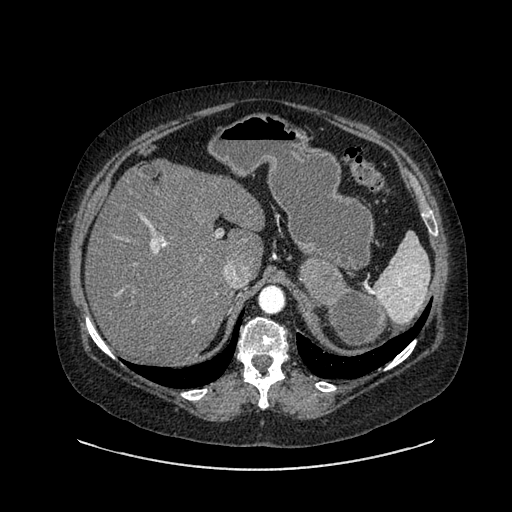
Contrast-enhanced abdominal CT, one axial slice; slice 621 of 769 in the series (ordered by position); 120 kVp; intravenous contrast given; soft-tissue window (W 400 / L 40 HU); 0.62 mm slice thickness; 512 × 512 image matrix, field of view 460 × 460 mm. Patient: female, 61 years. Case-level facts recorded for this patient, not image findings: diagnosis: adrenocortical carcinoma; tumour side: left adrenal; tumour size at pathology: 13 cm; Ki-67 index: 79 %; stage (as recorded): 2.
Structures marked on this image (semi-automatic segmentation, software-assisted and operator-edited):
- mass: box from (x=300, y=260) to (x=388, y=347) px